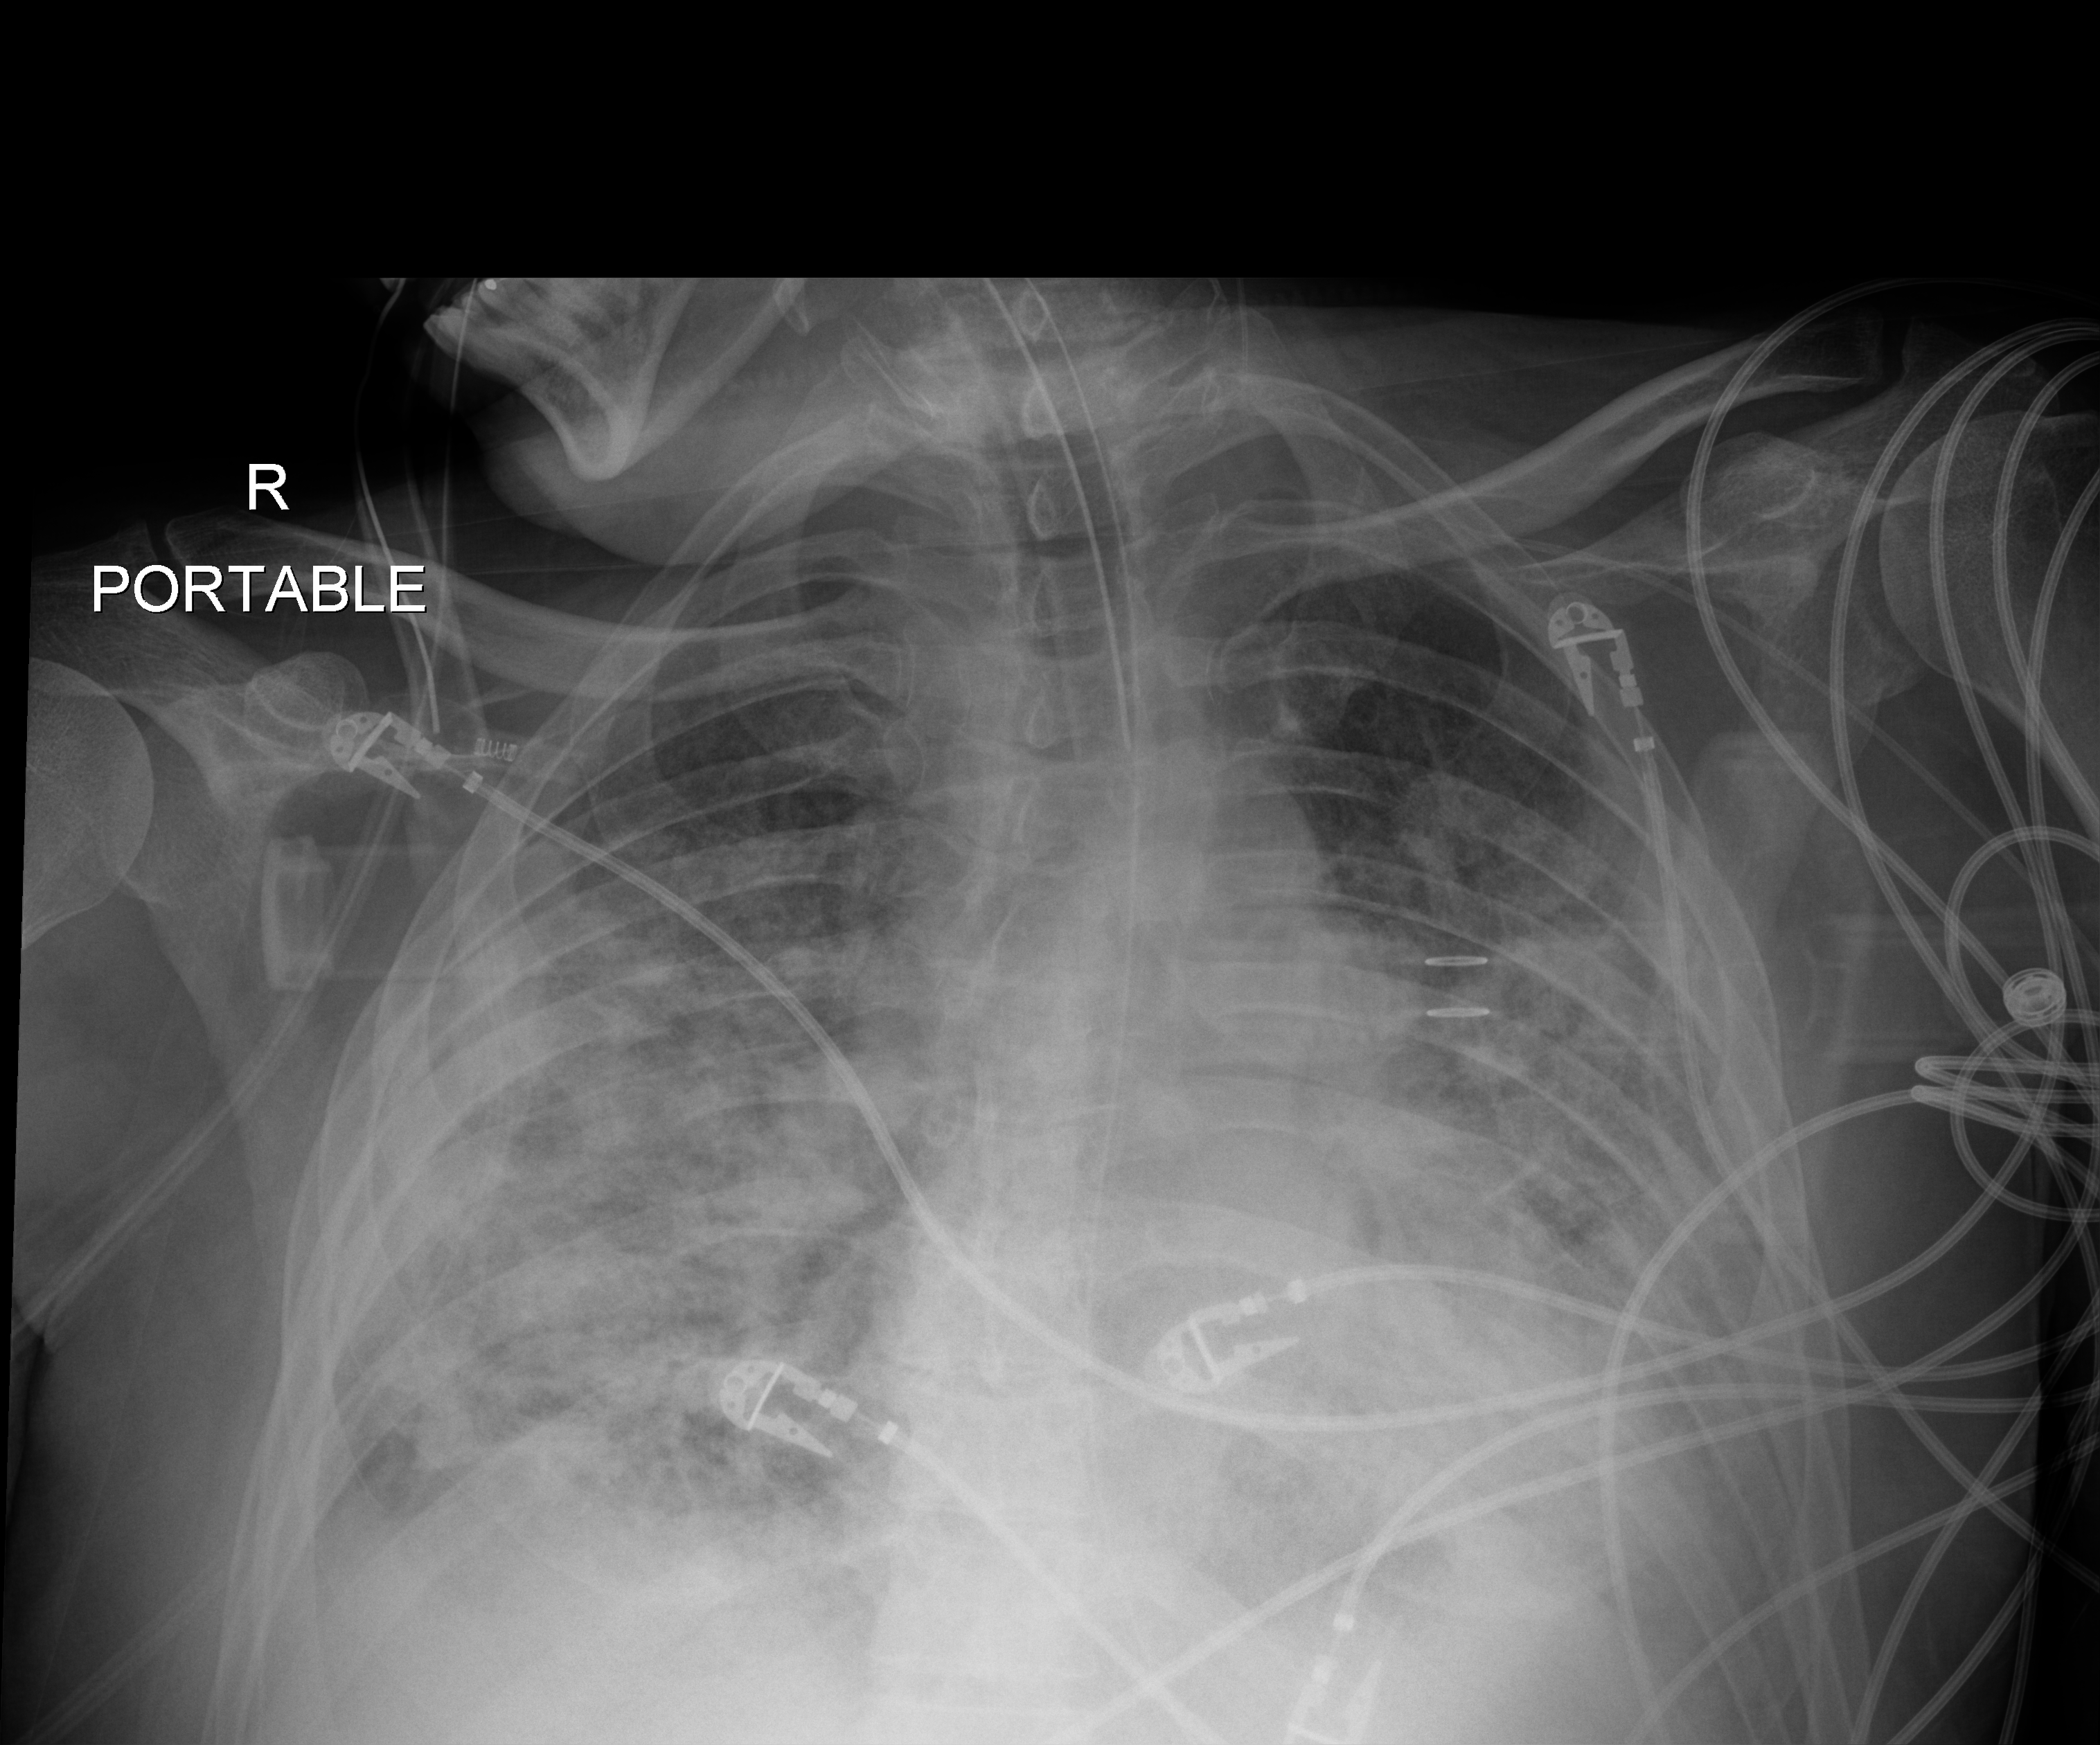
Bedside chest radiograph (digital radiography), anteroposterior (AP) projection. Patient hospitalised with COVID-19; male, aged 18–59 years.
From the hospital-stay record, not from the radiograph (when in the stay this image was taken is not recorded):
- mechanically ventilated during this hospital stay: yes
- admitted to intensive care during this hospital stay: yes